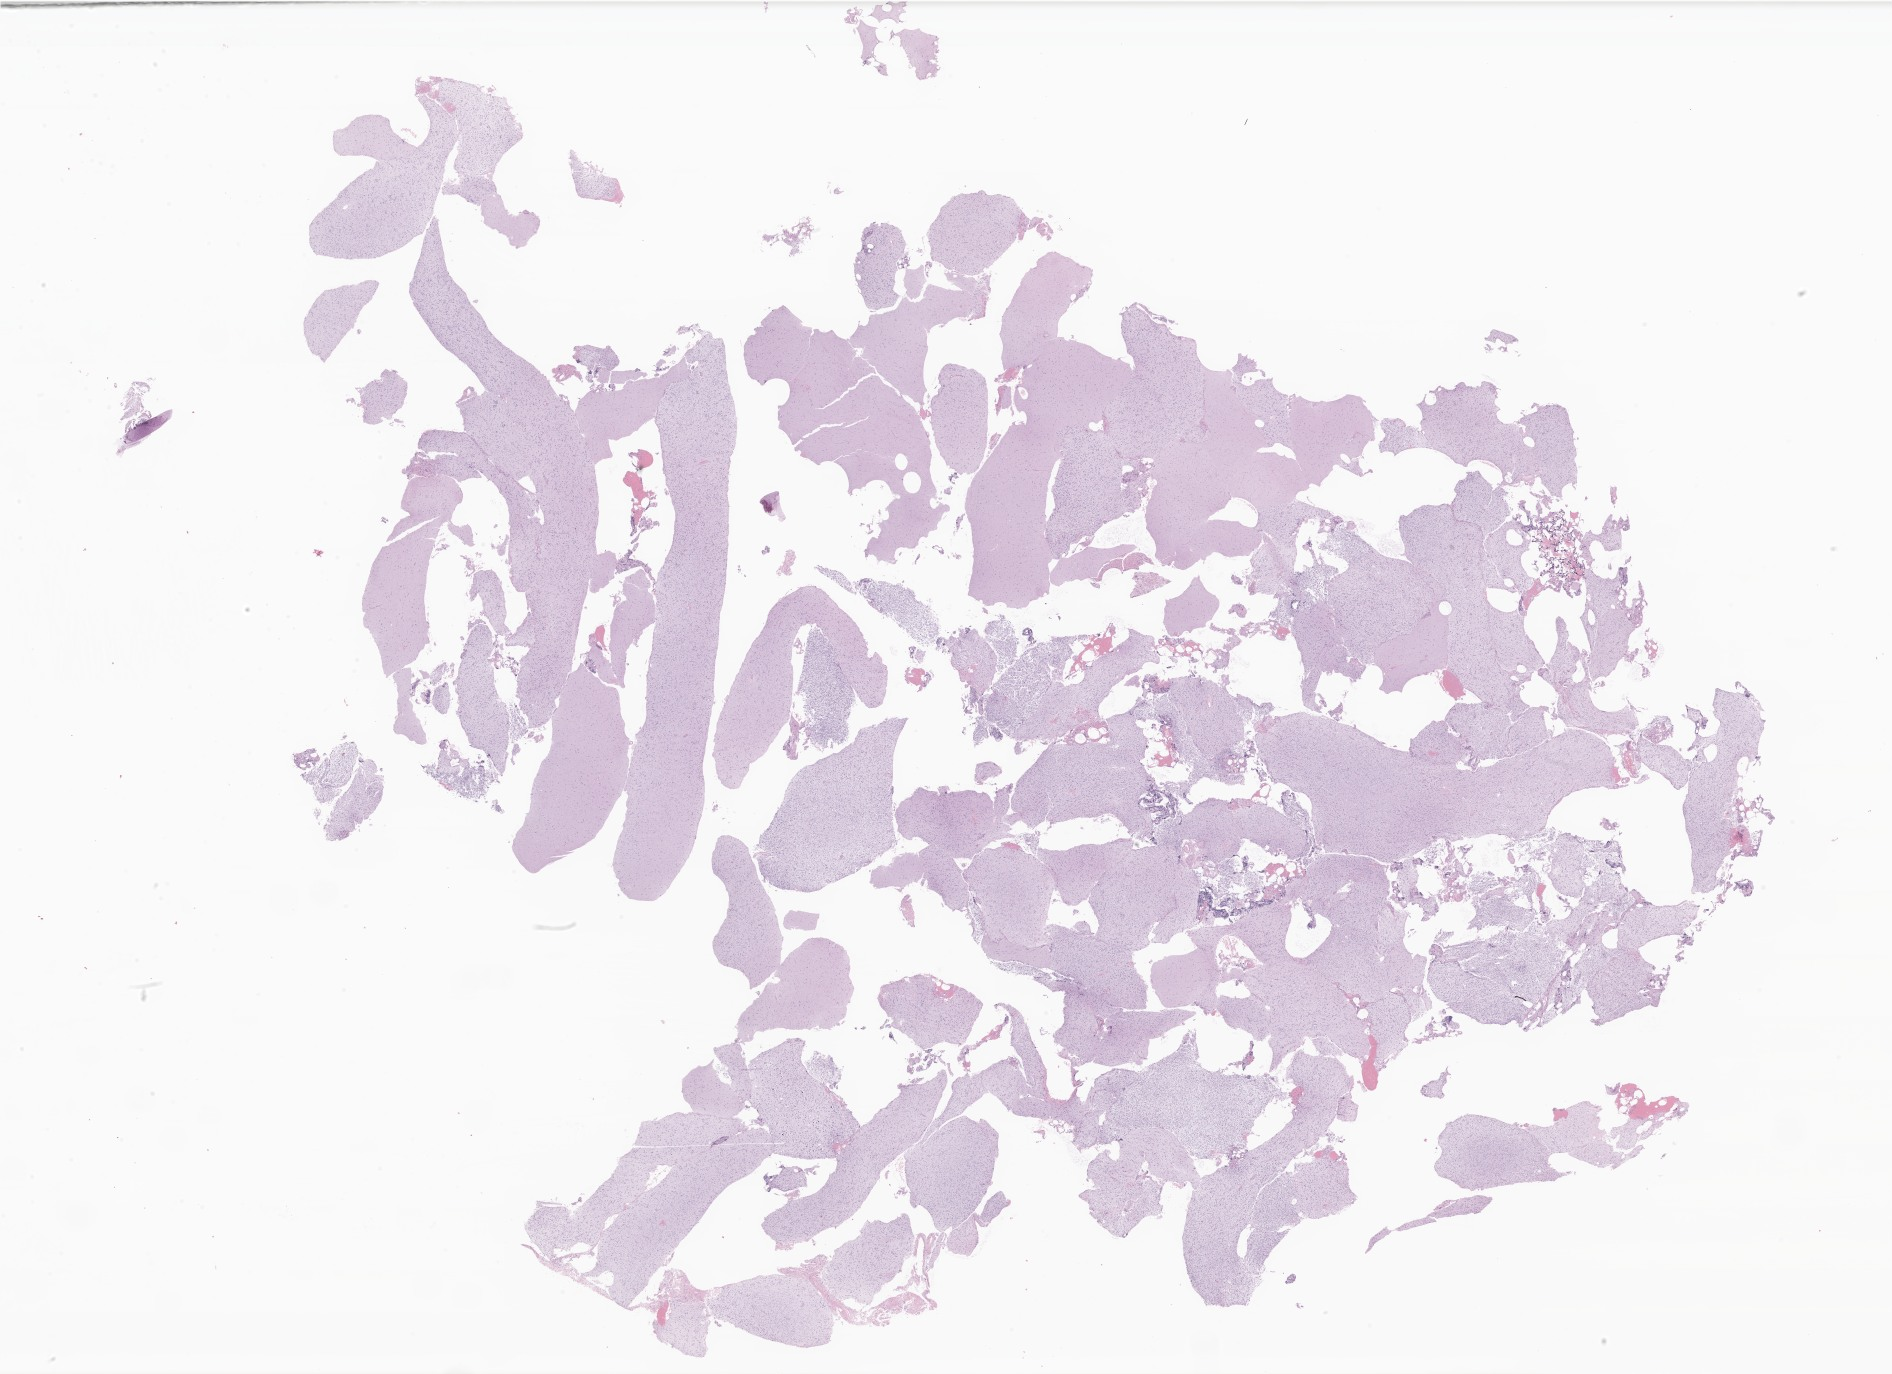
Whole-slide image, haematoxylin and eosin stain of tumor tissue from the brain, whole scanned area (about 31.9 x 23.2 mm) shown as a low-resolution overview; formalin-fixed paraffin-embedded section. Patient: male, age 155 months (12 years 11 months).
• diagnosis (ICD-O-3 morphology term): Neoplasm, uncertain whether benign or malignant